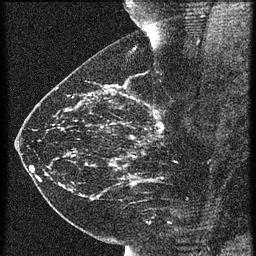
Breast MRI (dynamic contrast-enhanced), one sagittal slice; slice 31 of 60 in the series (ordered by position); 3 images stored at this slice position (order not interpretable as contrast timing); 1.5 T; TE 4.2 ms, TR 21.3 ms; 1.5 mm slice thickness; 256 × 256 image matrix, field of view 180 × 180 mm. Female patient, age 43 years. Case-level facts recorded for this patient, not image findings: setting: breast cancer imaged before/during neoadjuvant chemotherapy; receptor status: HER2-positive.
Annotated regions visible in this slice (semi-automatically segmented with operator editing):
- analysis volume of interest (the breast-tissue region the enhancement analysis was run in; not a lesion): box from (x=119, y=114) to (x=189, y=173) px
- tumour enhancement mask (voxels above the 90 % enhancement threshold inside the analysis volume of interest): (x=119, y=116)–(x=164, y=169)